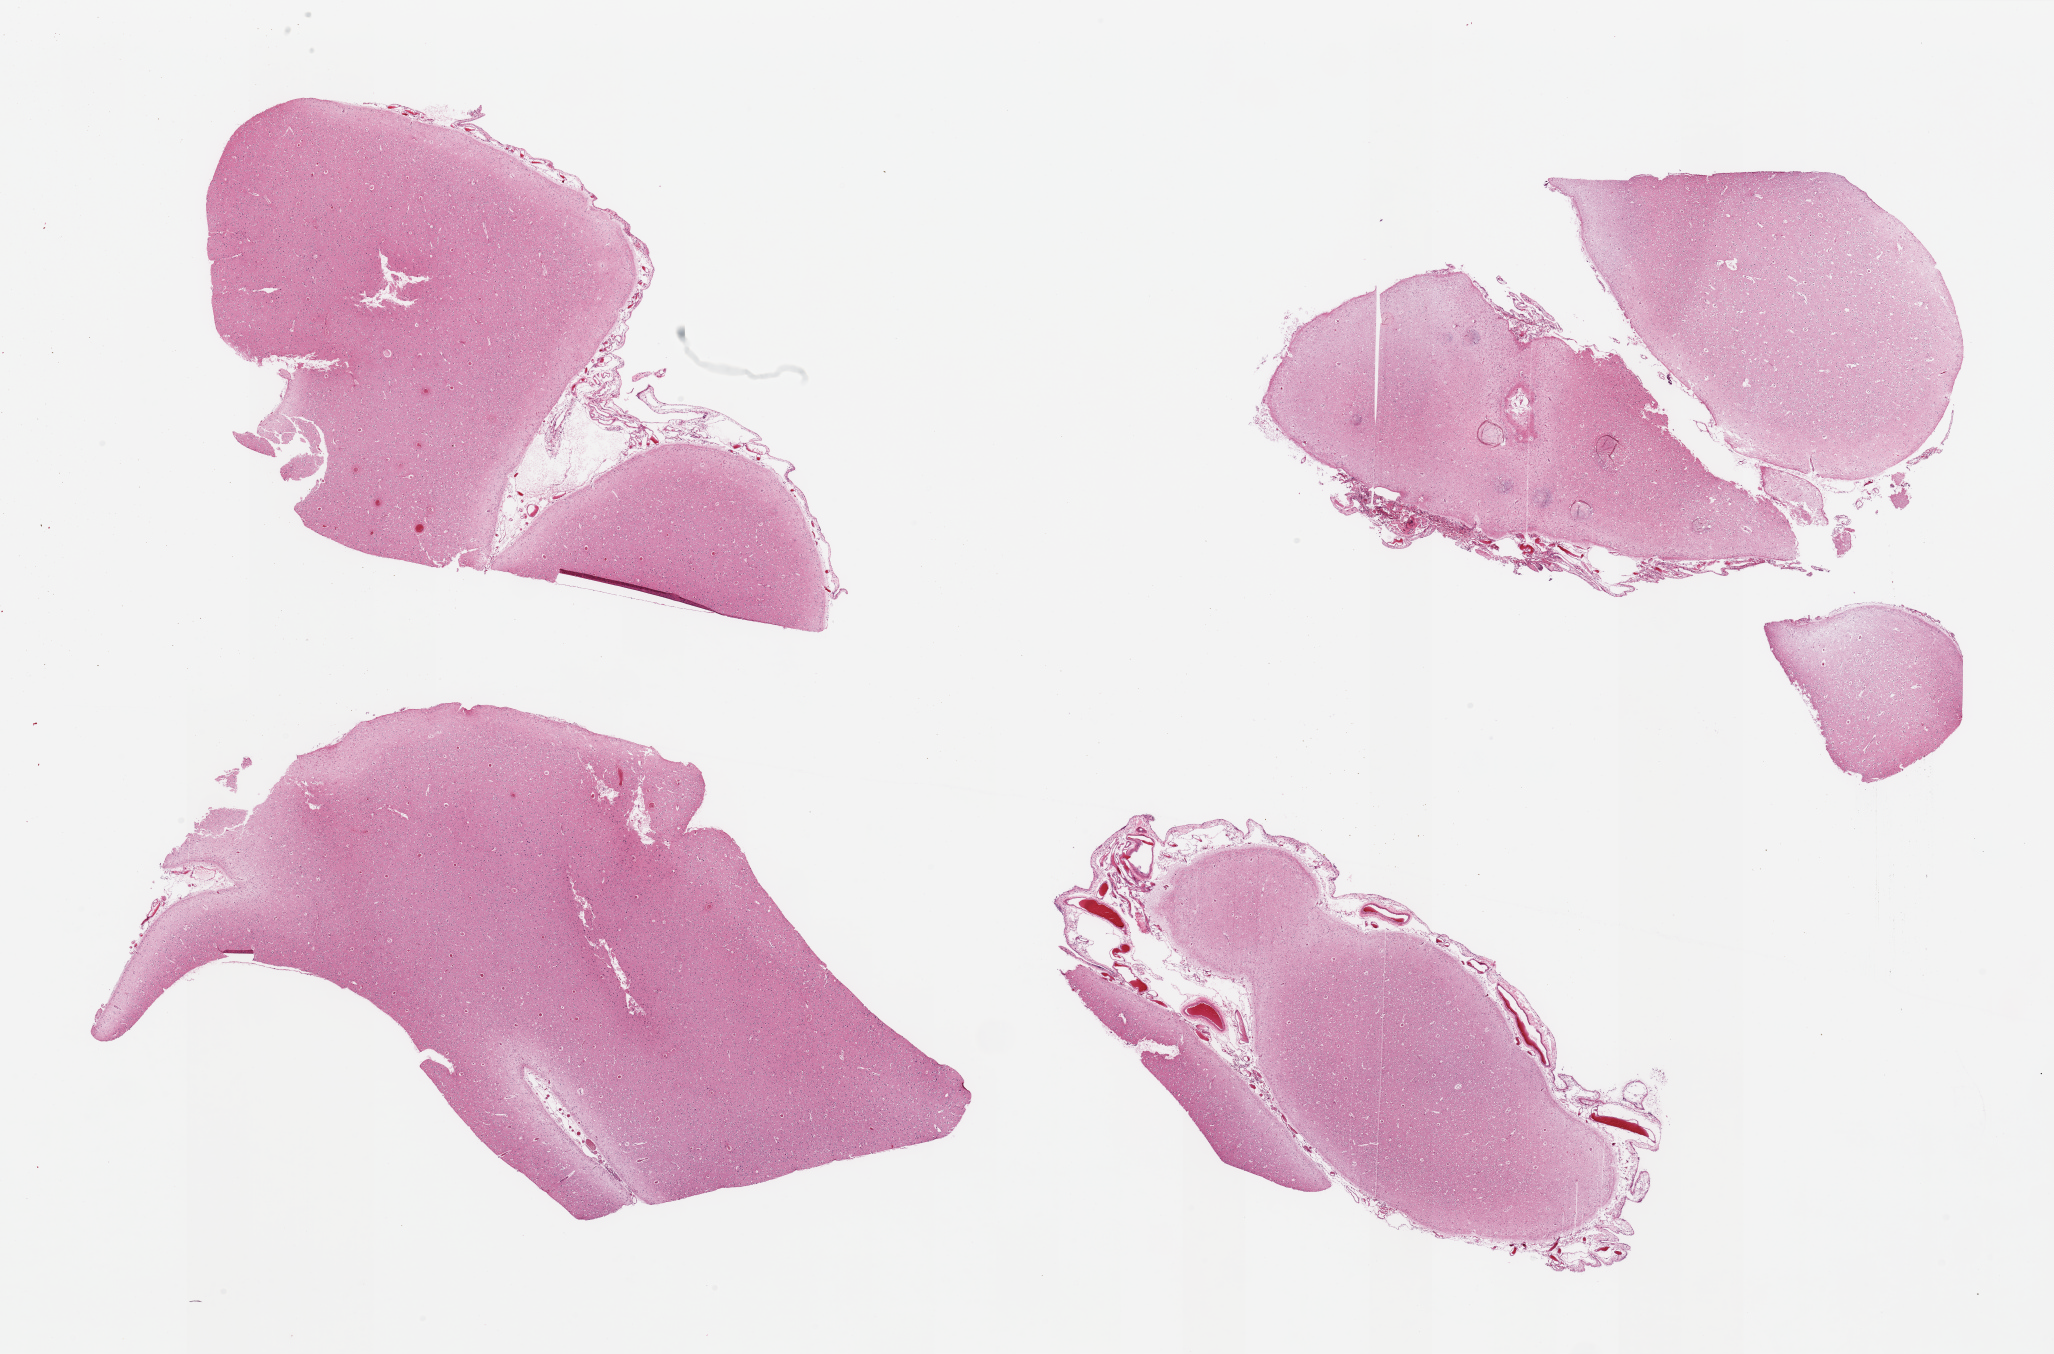
Digitized hematoxylin and eosin (H&E)-stained section — whole scanned area (about 32.5 x 21.4 mm) shown as a low-resolution overview; PAXgene-fixed, paraffin-embedded tissue; sampled site (target tissue): cerebral cortex; donor tissue sample. Donor sex: male.
Pathologist's review note for this sample: 4 pieces (fragmented); no abnormalities.